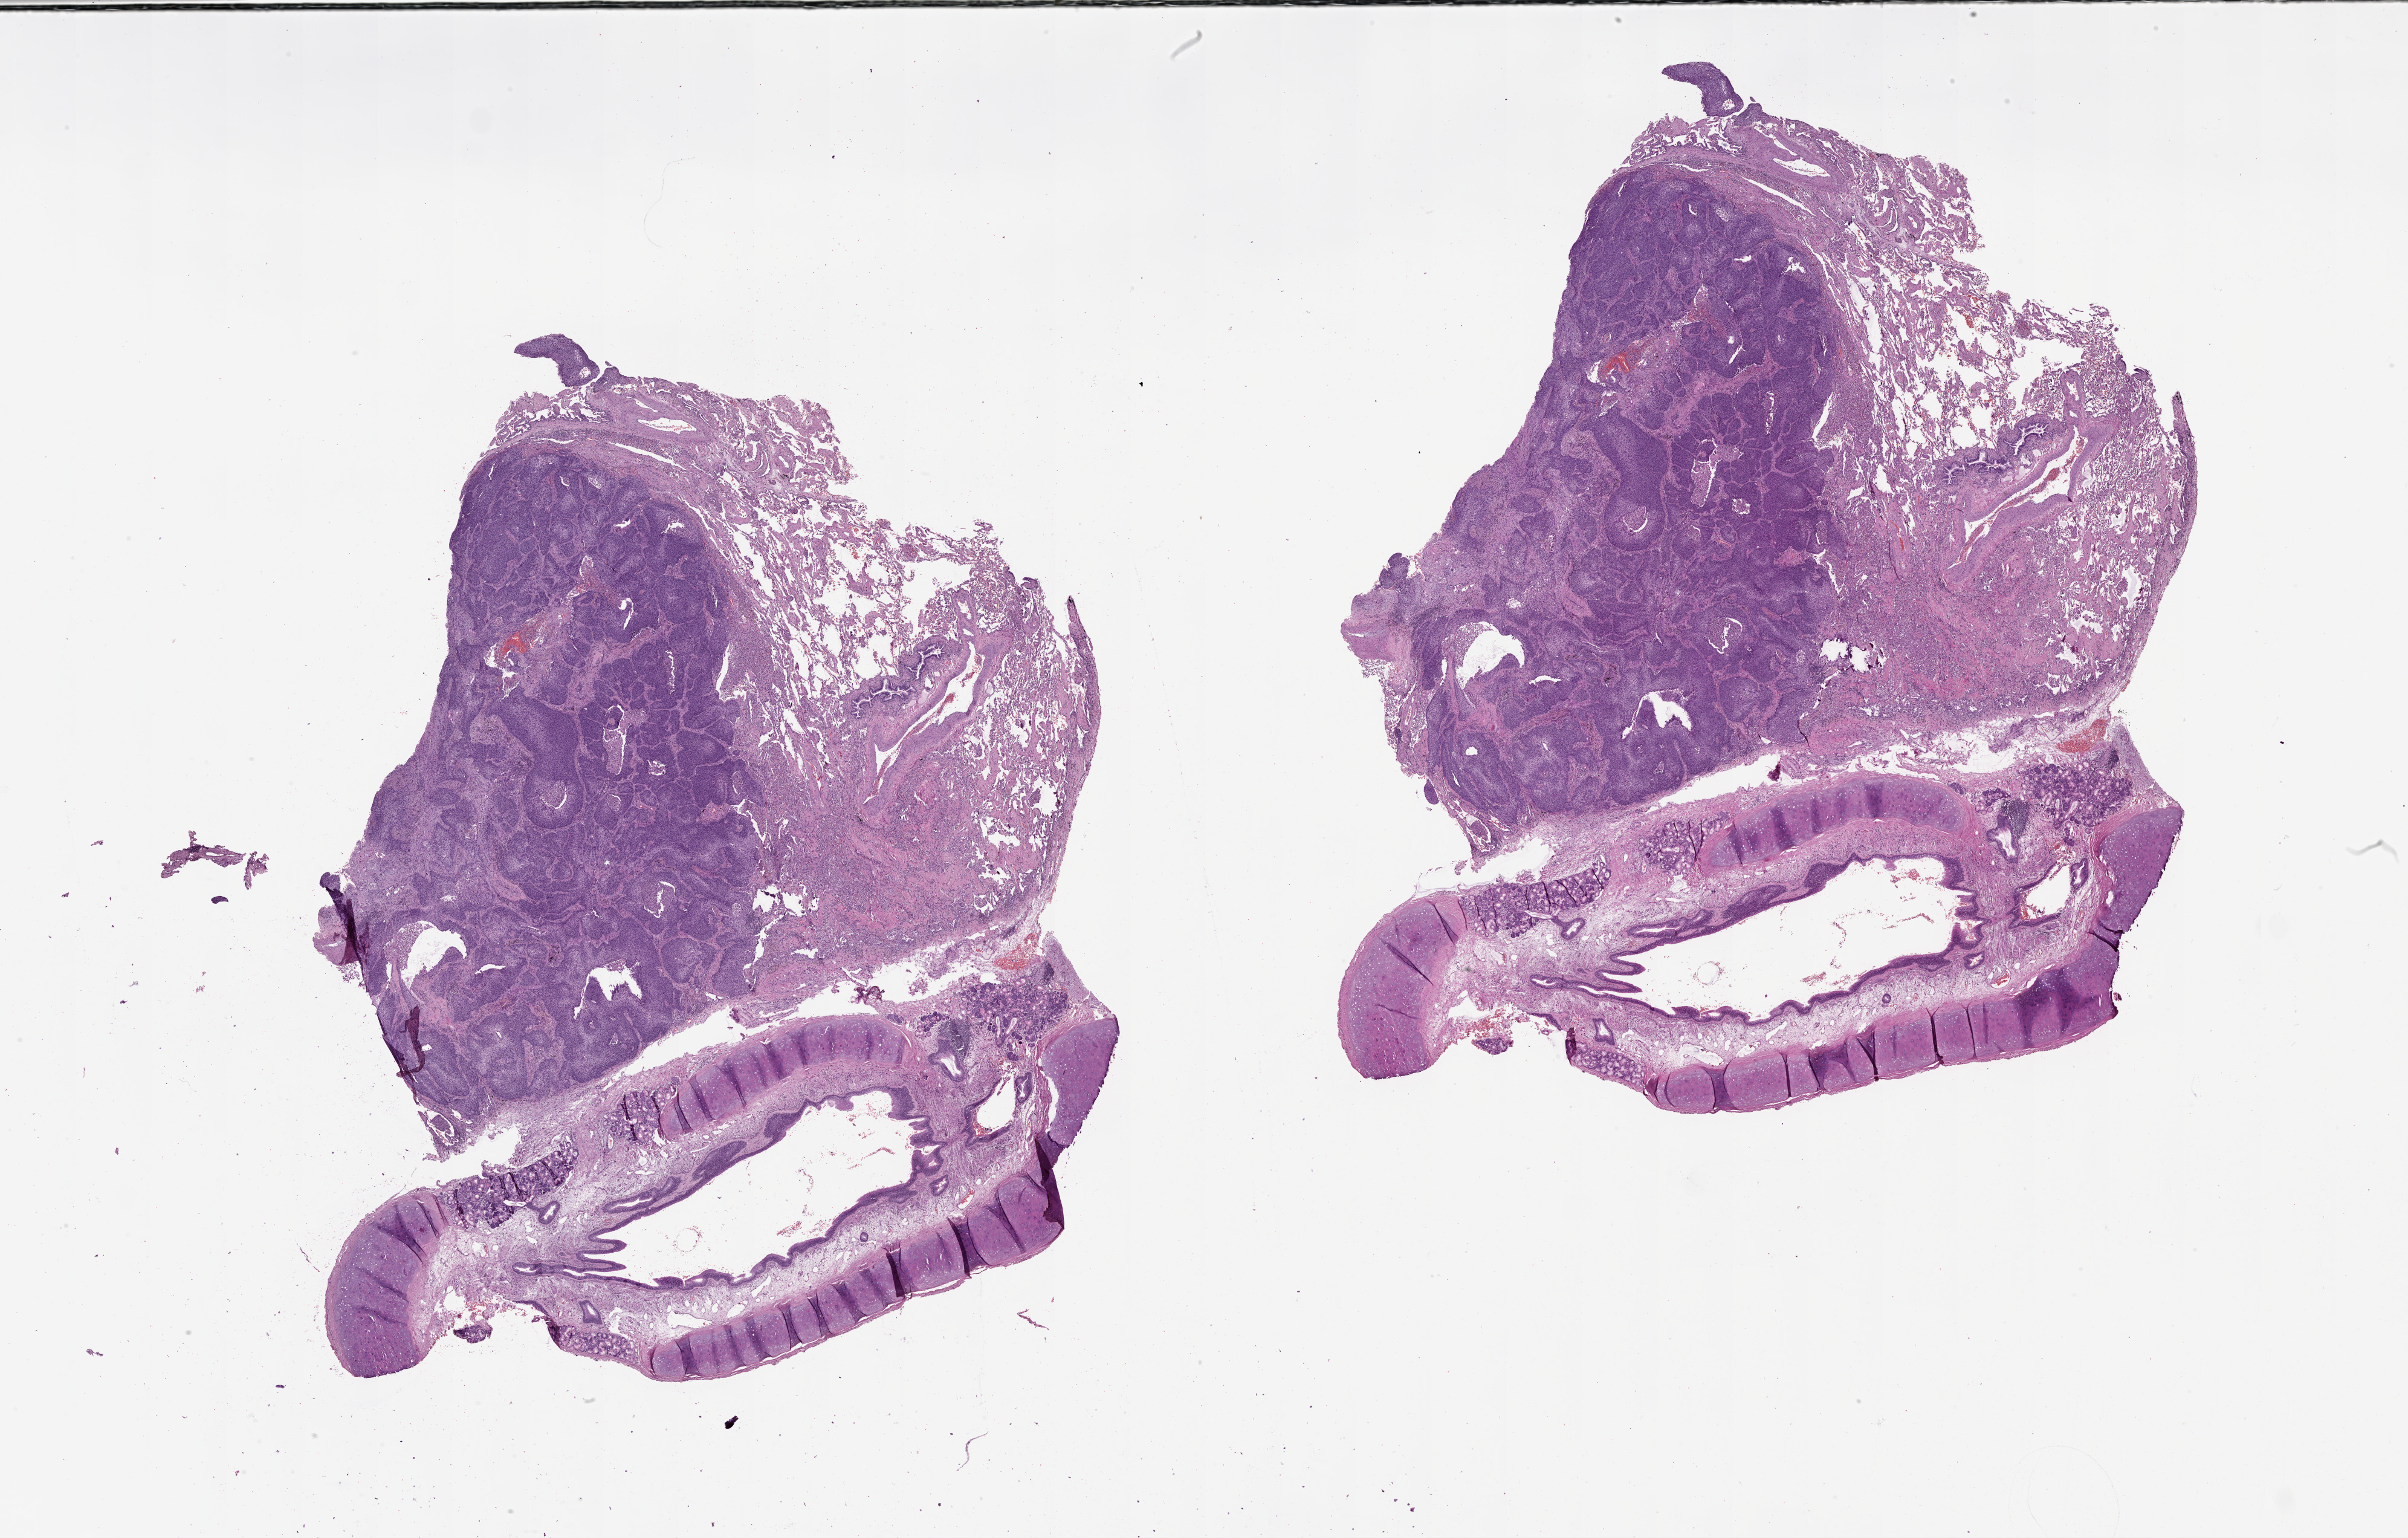
Whole-slide histology image, H&E, shown as a low-resolution overview of the whole scanned area (about 32.1 x 20.5 mm), lung, tumour tissue. 67-year-old male patient.
* patient diagnosis (cohort enrolment): squamous cell carcinoma (lung)